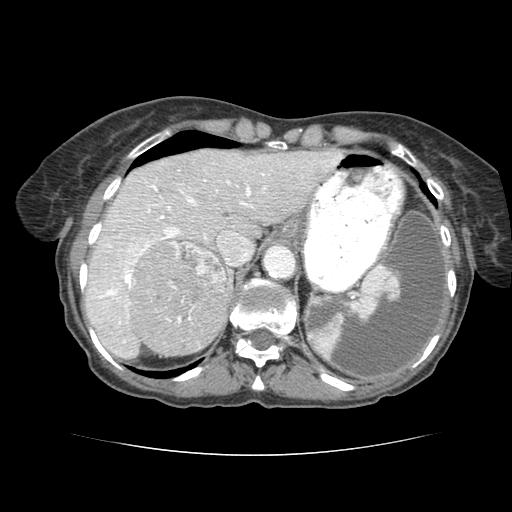
Contrast-enhanced abdominal CT (liver protocol), one axial slice; position 59 of 77 along the scan axis; 120 kVp; soft-tissue window (W 400 / L 40 HU); 512 × 512 image matrix, field of view 340 × 340 mm. From the clinical record (not read from this slice): diagnosis: hepatocellular carcinoma (patient treated with transarterial chemoembolisation; whether this scan precedes or follows treatment is not stated here); TNM stage (as recorded): Stage-I; Child-Pugh class: A; tumour size: 7.6 cm.
Outlined on this slice (semi-automatically segmented with operator editing):
- liver parenchyma outside the tumour (the mass and vessels are separate outlines, so this box may not span the whole liver): box from (x=80, y=146) to (x=336, y=352) px
- mass: (x=127, y=237)–(x=229, y=352)
- liver vessels: (x=80, y=177)–(x=303, y=338)